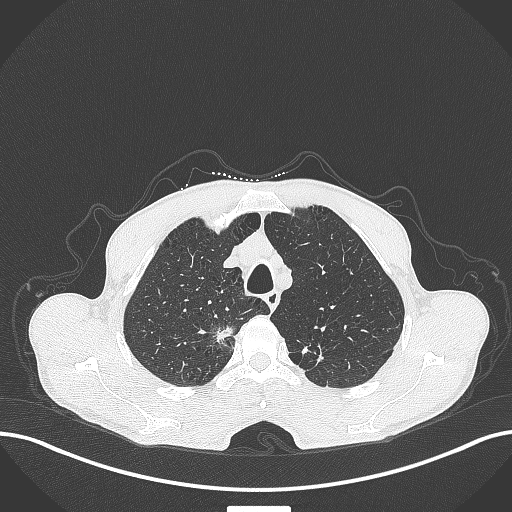
Chest CT, one axial slice; position 350 of 445 along the scan axis; 120 kVp; lung window (W 1500 / L -600 HU); 512 × 512 image matrix, field of view 400 × 400 mm. Male patient, age 70 years. From the clinical record (not read from this slice): clinical TNM (as recorded): T1a N0 M0.
Annotated regions visible in this slice (rectangle marked by the reading radiologist):
- lung tumour (recorded histology: adenocarcinoma): bounding box [x1, y1, x2, y2] px = [213, 321, 238, 352]